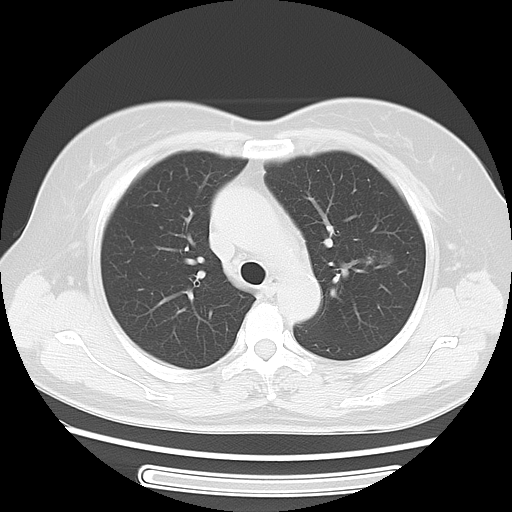
Chest CT, one axial slice. Slice 34 of 52 in the series (ordered by position). Reconstruction kernel LUNG. Lung window (W 1500 / L -600 HU). 512 × 512 image matrix, field of view 350 × 350 mm. Patient: female, 54 years. Case-level facts recorded for this patient, not image findings: clinical TNM (as recorded): T1c N0 M0.
Annotated regions visible in this slice (bounding box drawn by a radiologist):
- lung tumour (recorded histology: adenocarcinoma): box from (x=356, y=236) to (x=397, y=278) px